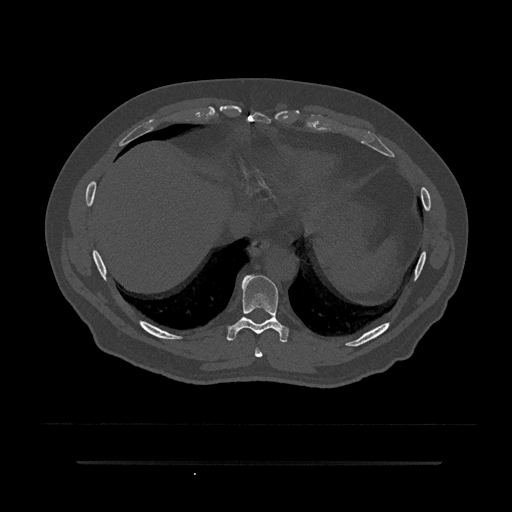
CT including the spine, one axial slice; slice 377 of 797 in the series (ordered by position); 120 kVp; bone window (W 1800 / L 400 HU); 0.5 mm slice thickness; 512 × 512 image matrix, field of view 464 × 464 mm. Male patient, age 59 years. From the clinical record (not read from this slice): primary cancer: bile ducts.
Structures marked on this image (semi-automatic segmentation, software-assisted and operator-edited):
- T8 vertebra: box from (x=255, y=348) to (x=263, y=358) px
- T9 vertebra: (x=226, y=275)–(x=289, y=343)